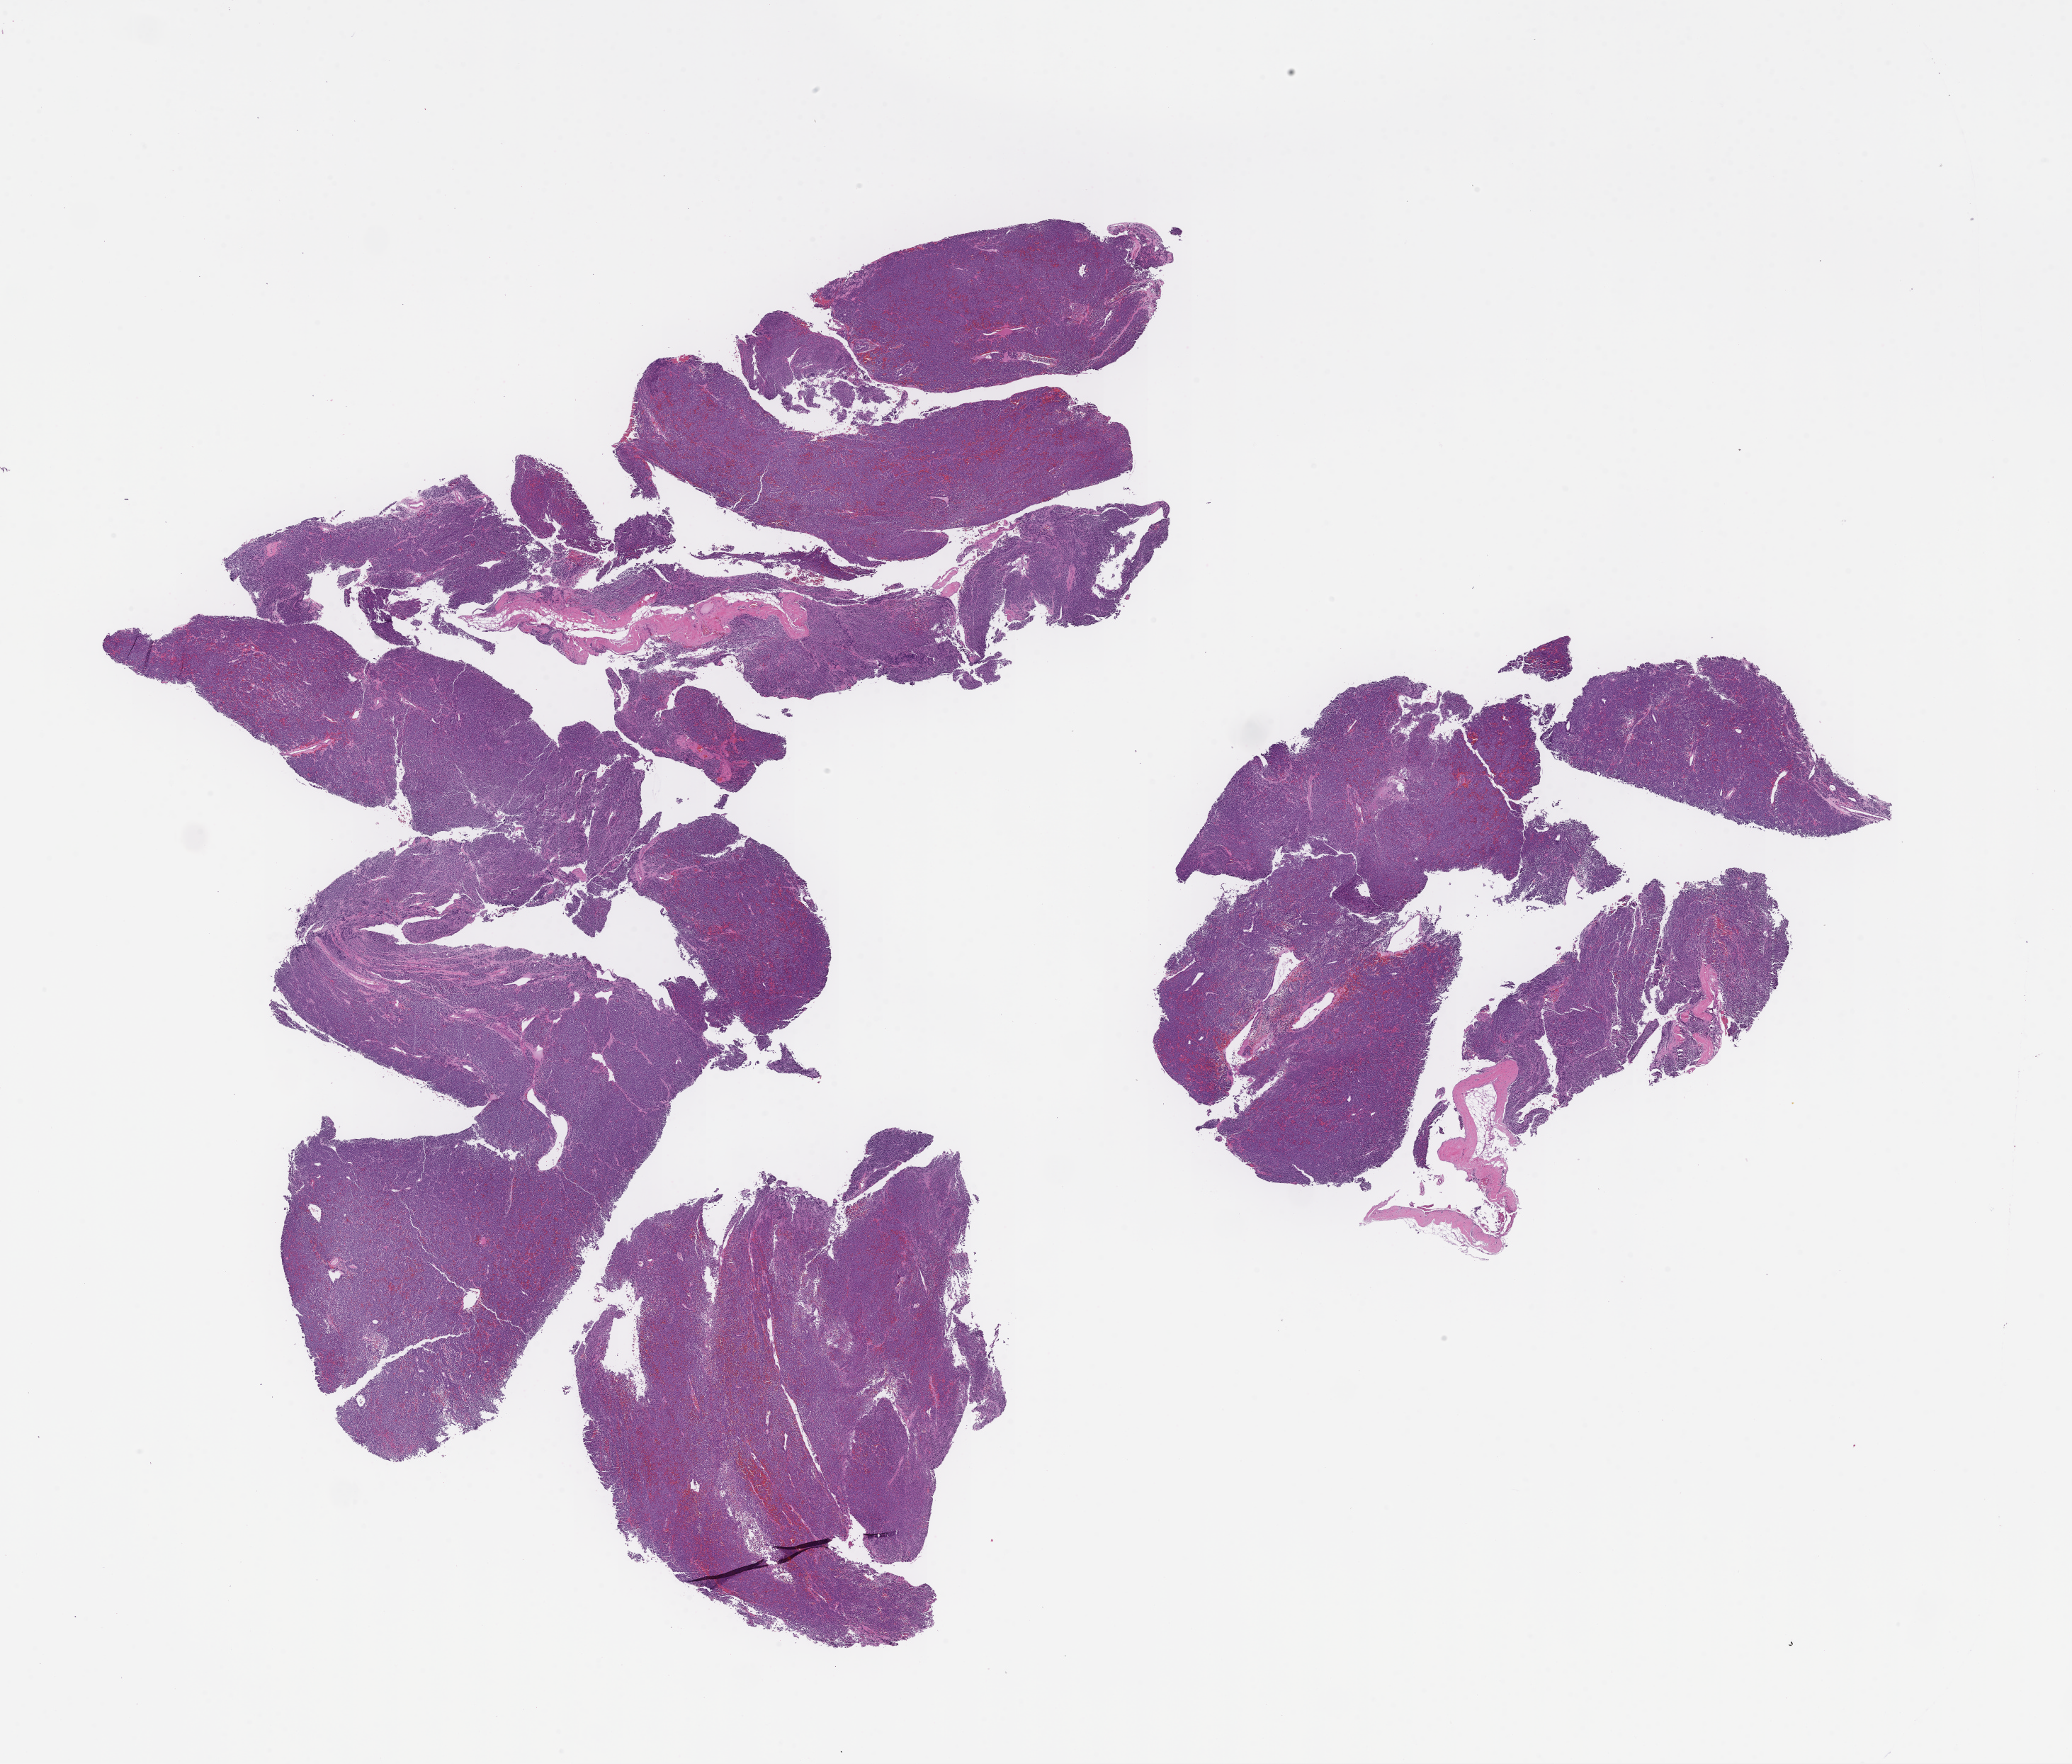
H&E whole-slide image, a low-resolution overview of the entire scanned area, about 23.6 x 20.1 mm, FFPE section, tissue site: bone marrow, archival tissue. Female patient.
This section: primary tumor. Diagnosis: Plasma Cell Myeloma.